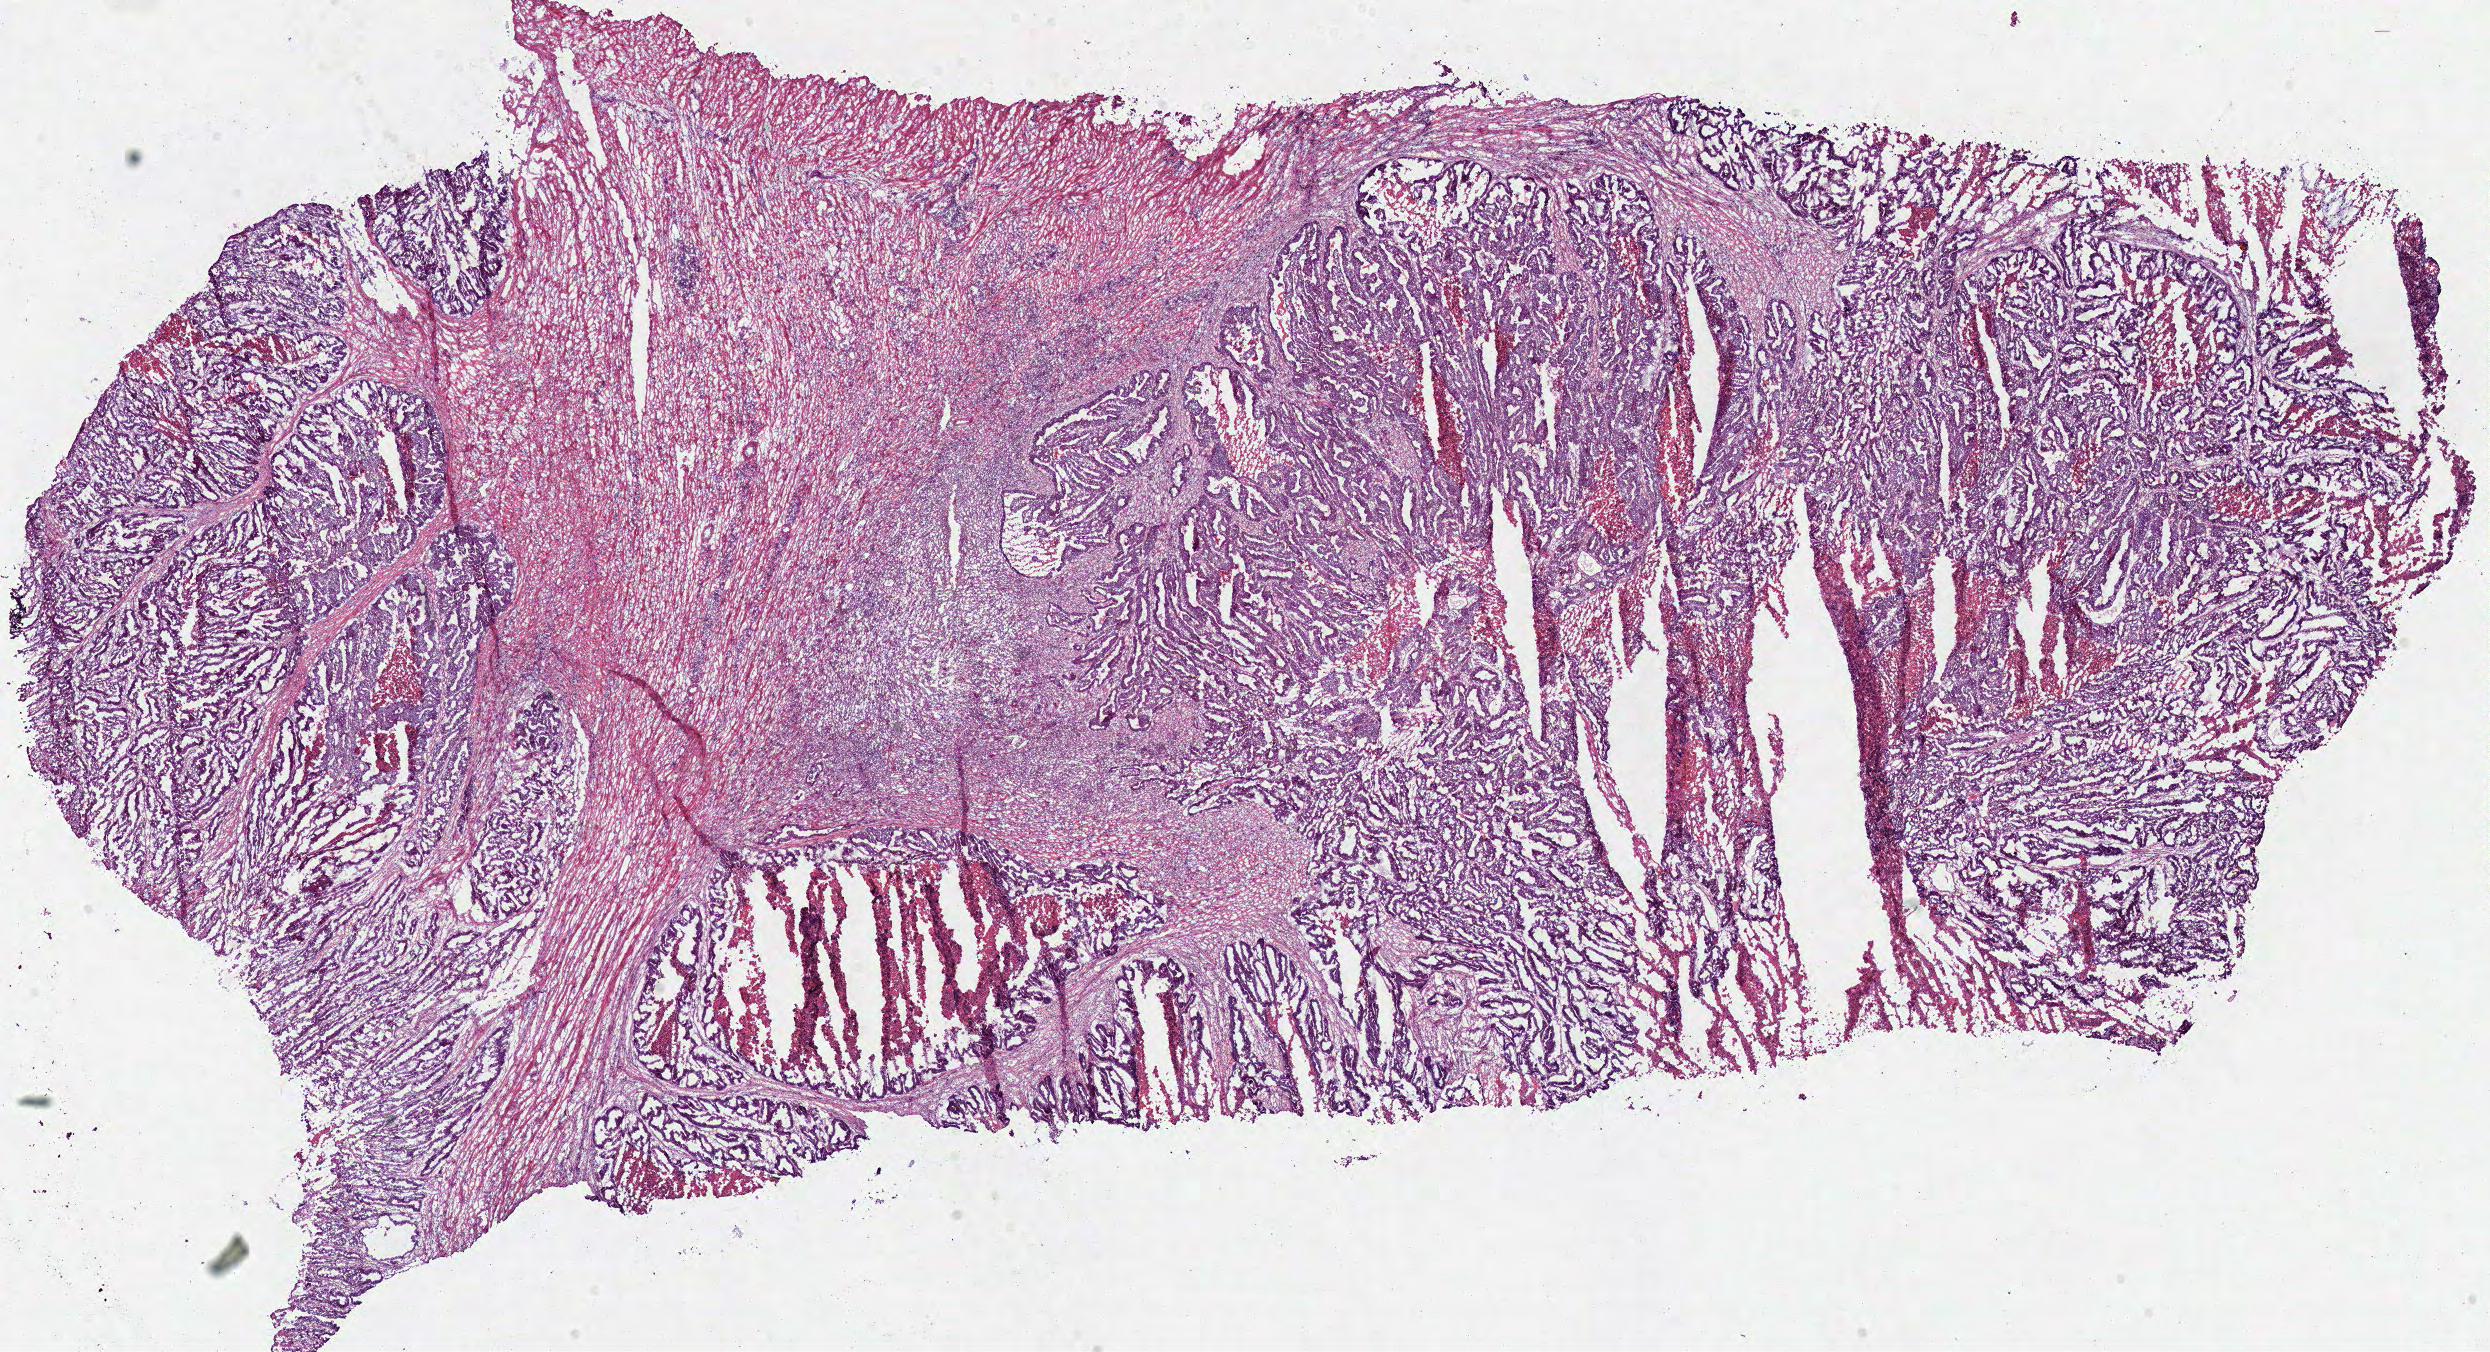
Whole-slide histology image, H&E — low-resolution overview of the scanned area, about 19.6 x 10.6 mm (from a 40x scan), frozen section, primary tumour sample from the colon. Male patient; age at initial diagnosis 63 years. Composition of this section per pathologist review: tumour cells 60%, tumour nuclei 70%, normal cells 0%, stromal cells 20%, necrosis 20%. Infiltration values recorded for this section: lymphocyte infiltration 10%, monocyte infiltration 5%, neutrophil infiltration 10%.
AJCC pathologic stage: IIIB (6th edition). TNM: T3 N1 M0. Lymph nodes positive (case pathology): 1 of 2 examined. Diagnosis: Papillary adenocarcinoma, NOS.